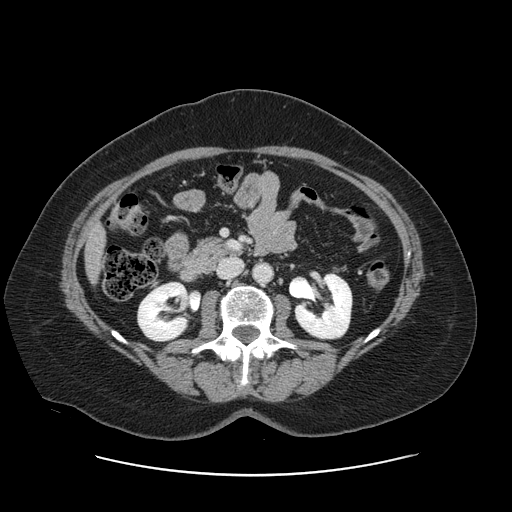
Contrast-enhanced abdominal CT, one axial slice; slice 45 of 161 in the series (ordered by position); 120 kVp; intravenous contrast given; soft-tissue window (W 400 / L 40 HU); 512 × 512 image matrix, field of view 398 × 398 mm. Female patient, age 62 years. Case-level facts recorded for this patient, not image findings: diagnosis: colorectal cancer liver metastases, imaged before liver resection; multiple liver metastases: no; largest metastasis: 2.5 cm.
Annotated regions visible in this slice (manually delineated by an expert):
- liver: bounding box [x1, y1, x2, y2] px = [87, 230, 104, 278]